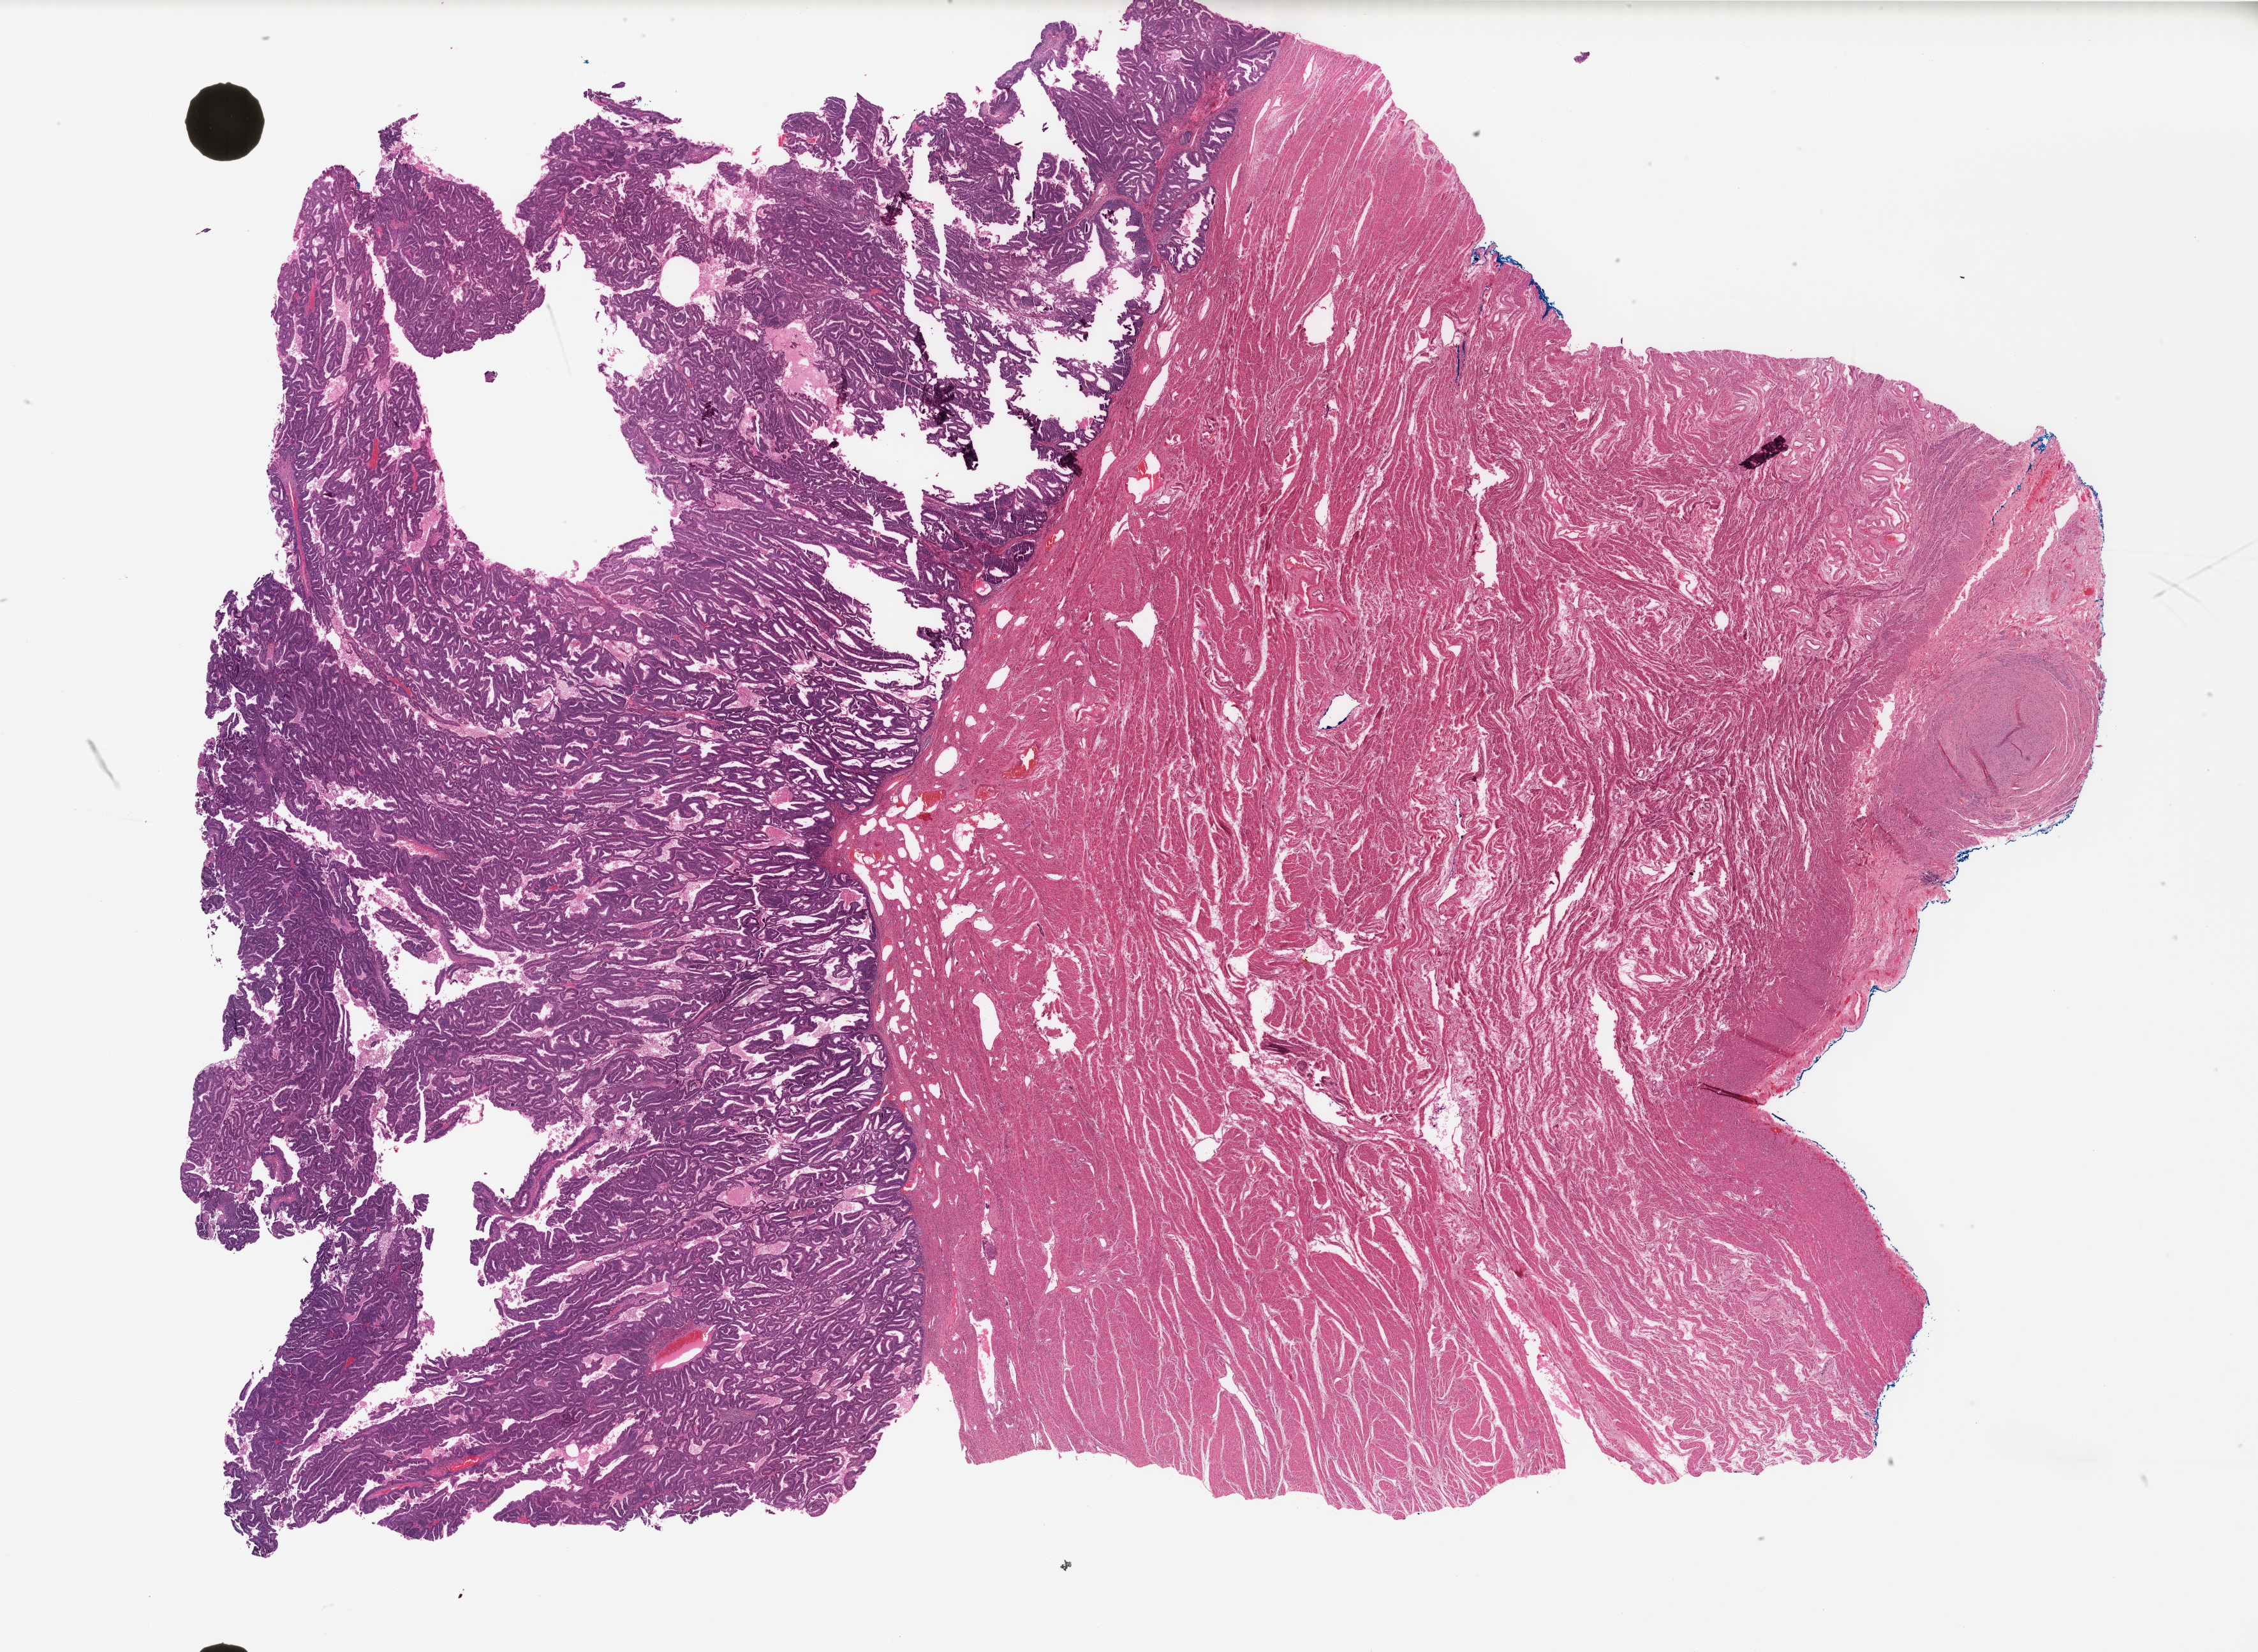
H&E whole-slide image — low-resolution overview of the scanned area, about 28.1 x 20.6 mm; FFPE section; primary tumour sample from the uterus. Patient: female, age at initial diagnosis 61 years. Histologic grade: G1 (well differentiated).
* histologic diagnosis: Endometrioid adenocarcinoma, NOS
* FIGO stage: IB
* lymph nodes positive (case pathology): 0 of 3 examined